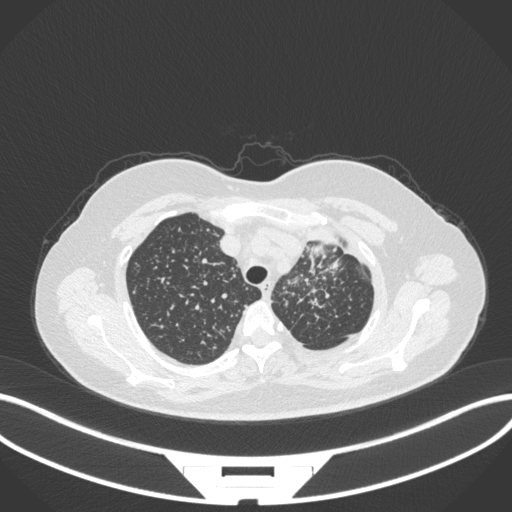
Chest CT, one axial slice; position 270 of 348 along the scan axis; reconstruction kernel B31f; 120 kVp; lung window (W 1500 / L -600 HU); 1 mm slice thickness; 512 × 512 image matrix. Female patient, age 49 years. From the clinical record (not read from this slice): clinical TNM (as recorded): T1c N0 M1.
Annotated regions visible in this slice (rectangle marked by the reading radiologist):
- lung tumour (recorded histology: adenocarcinoma): bounding box [x1, y1, x2, y2] px = [307, 228, 344, 250]